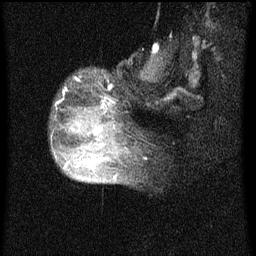
Breast MRI (dynamic contrast-enhanced), one sagittal slice; position 17 of 60 along the scan axis; dynamic contrast-enhanced series, image 2 of 4 at this slice position (ordered by acquisition); 1.5 T; TE 4.2 ms, TR 8 ms; 2 mm slice thickness; 256 × 256 image matrix. Female patient, age 50 years.
Outlined on this slice (semi-automatic segmentation, software-assisted and operator-edited):
- analysis volume of interest (the breast-tissue region the enhancement analysis was run in; not a lesion): box from (x=54, y=98) to (x=124, y=177) px
- tumour enhancement mask (voxels above the 70 % enhancement threshold inside the analysis volume of interest): (x=65, y=128)–(x=103, y=169)